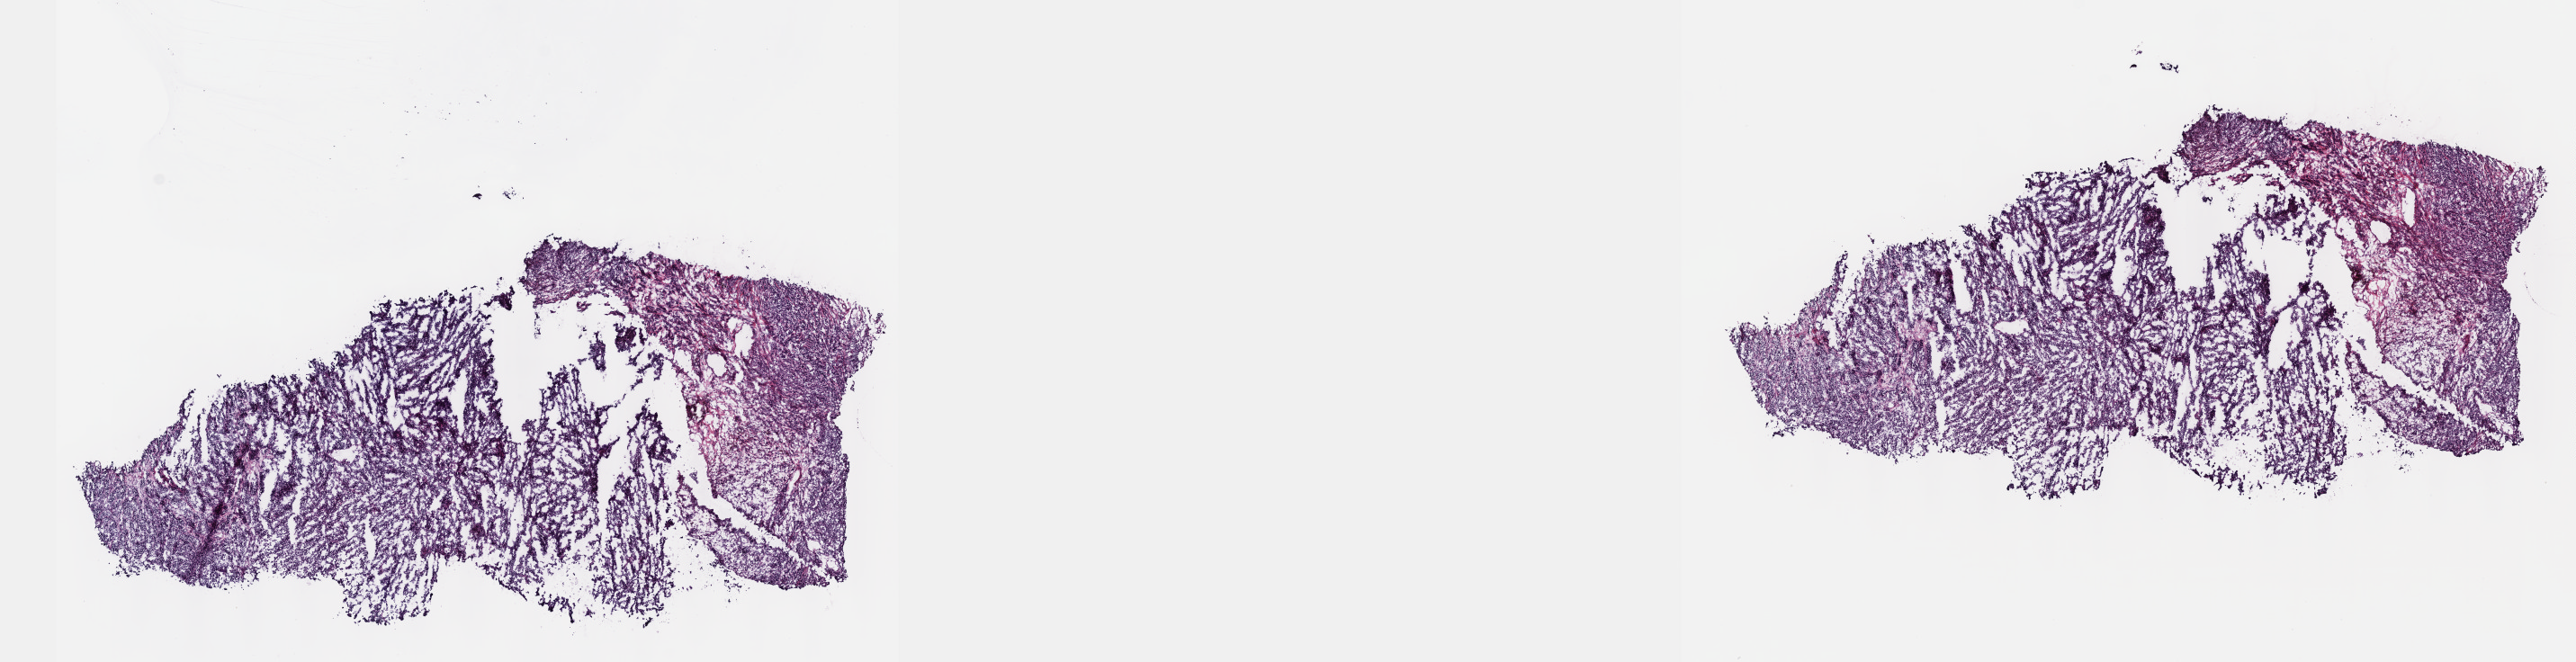
Hematoxylin and eosin (H&E) stained whole-slide image — whole scanned area (about 23.1 x 5.9 mm, from a 40x scan) shown as a low-resolution overview; frozen section from the top of the tissue portion; sample: primary tumour, skin. Male patient; age at initial diagnosis 68 years.
Diagnosis: Malignant melanoma, NOS.